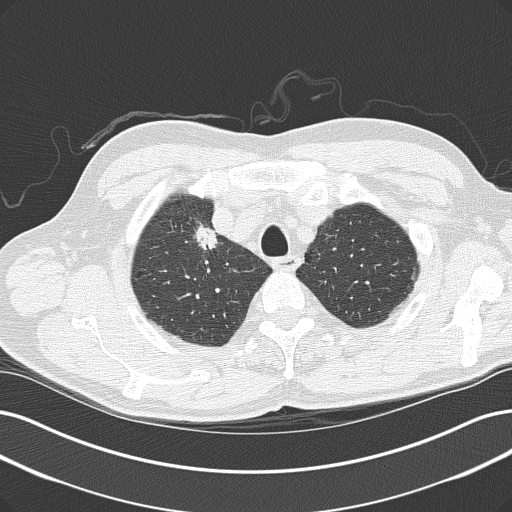
Chest CT (low-dose screening protocol), one axial image. Baseline screening round. Lung window (W 1500 / L -600 HU). 2 mm slice thickness. Slice 28 of 152 in the series. 512 × 512 image matrix. Male, age 61 years at enrolment. Current smoker at enrolment.
Expert reader's lesion annotation, bounding box [x1, y1, x2, y2] px = [191, 223, 246, 269]. The screening reader recorded 2 non-calcified nodules or masses ≥4 mm on this exam (right upper lobe, right upper lobe); which of them this box marks is not recorded. Later outcome: lung cancer diagnosed 54 days after this screen — adenocarcinoma, NOS, right upper lobe, poorly differentiated (G3), stage IIIB (AJCC 6th edition).